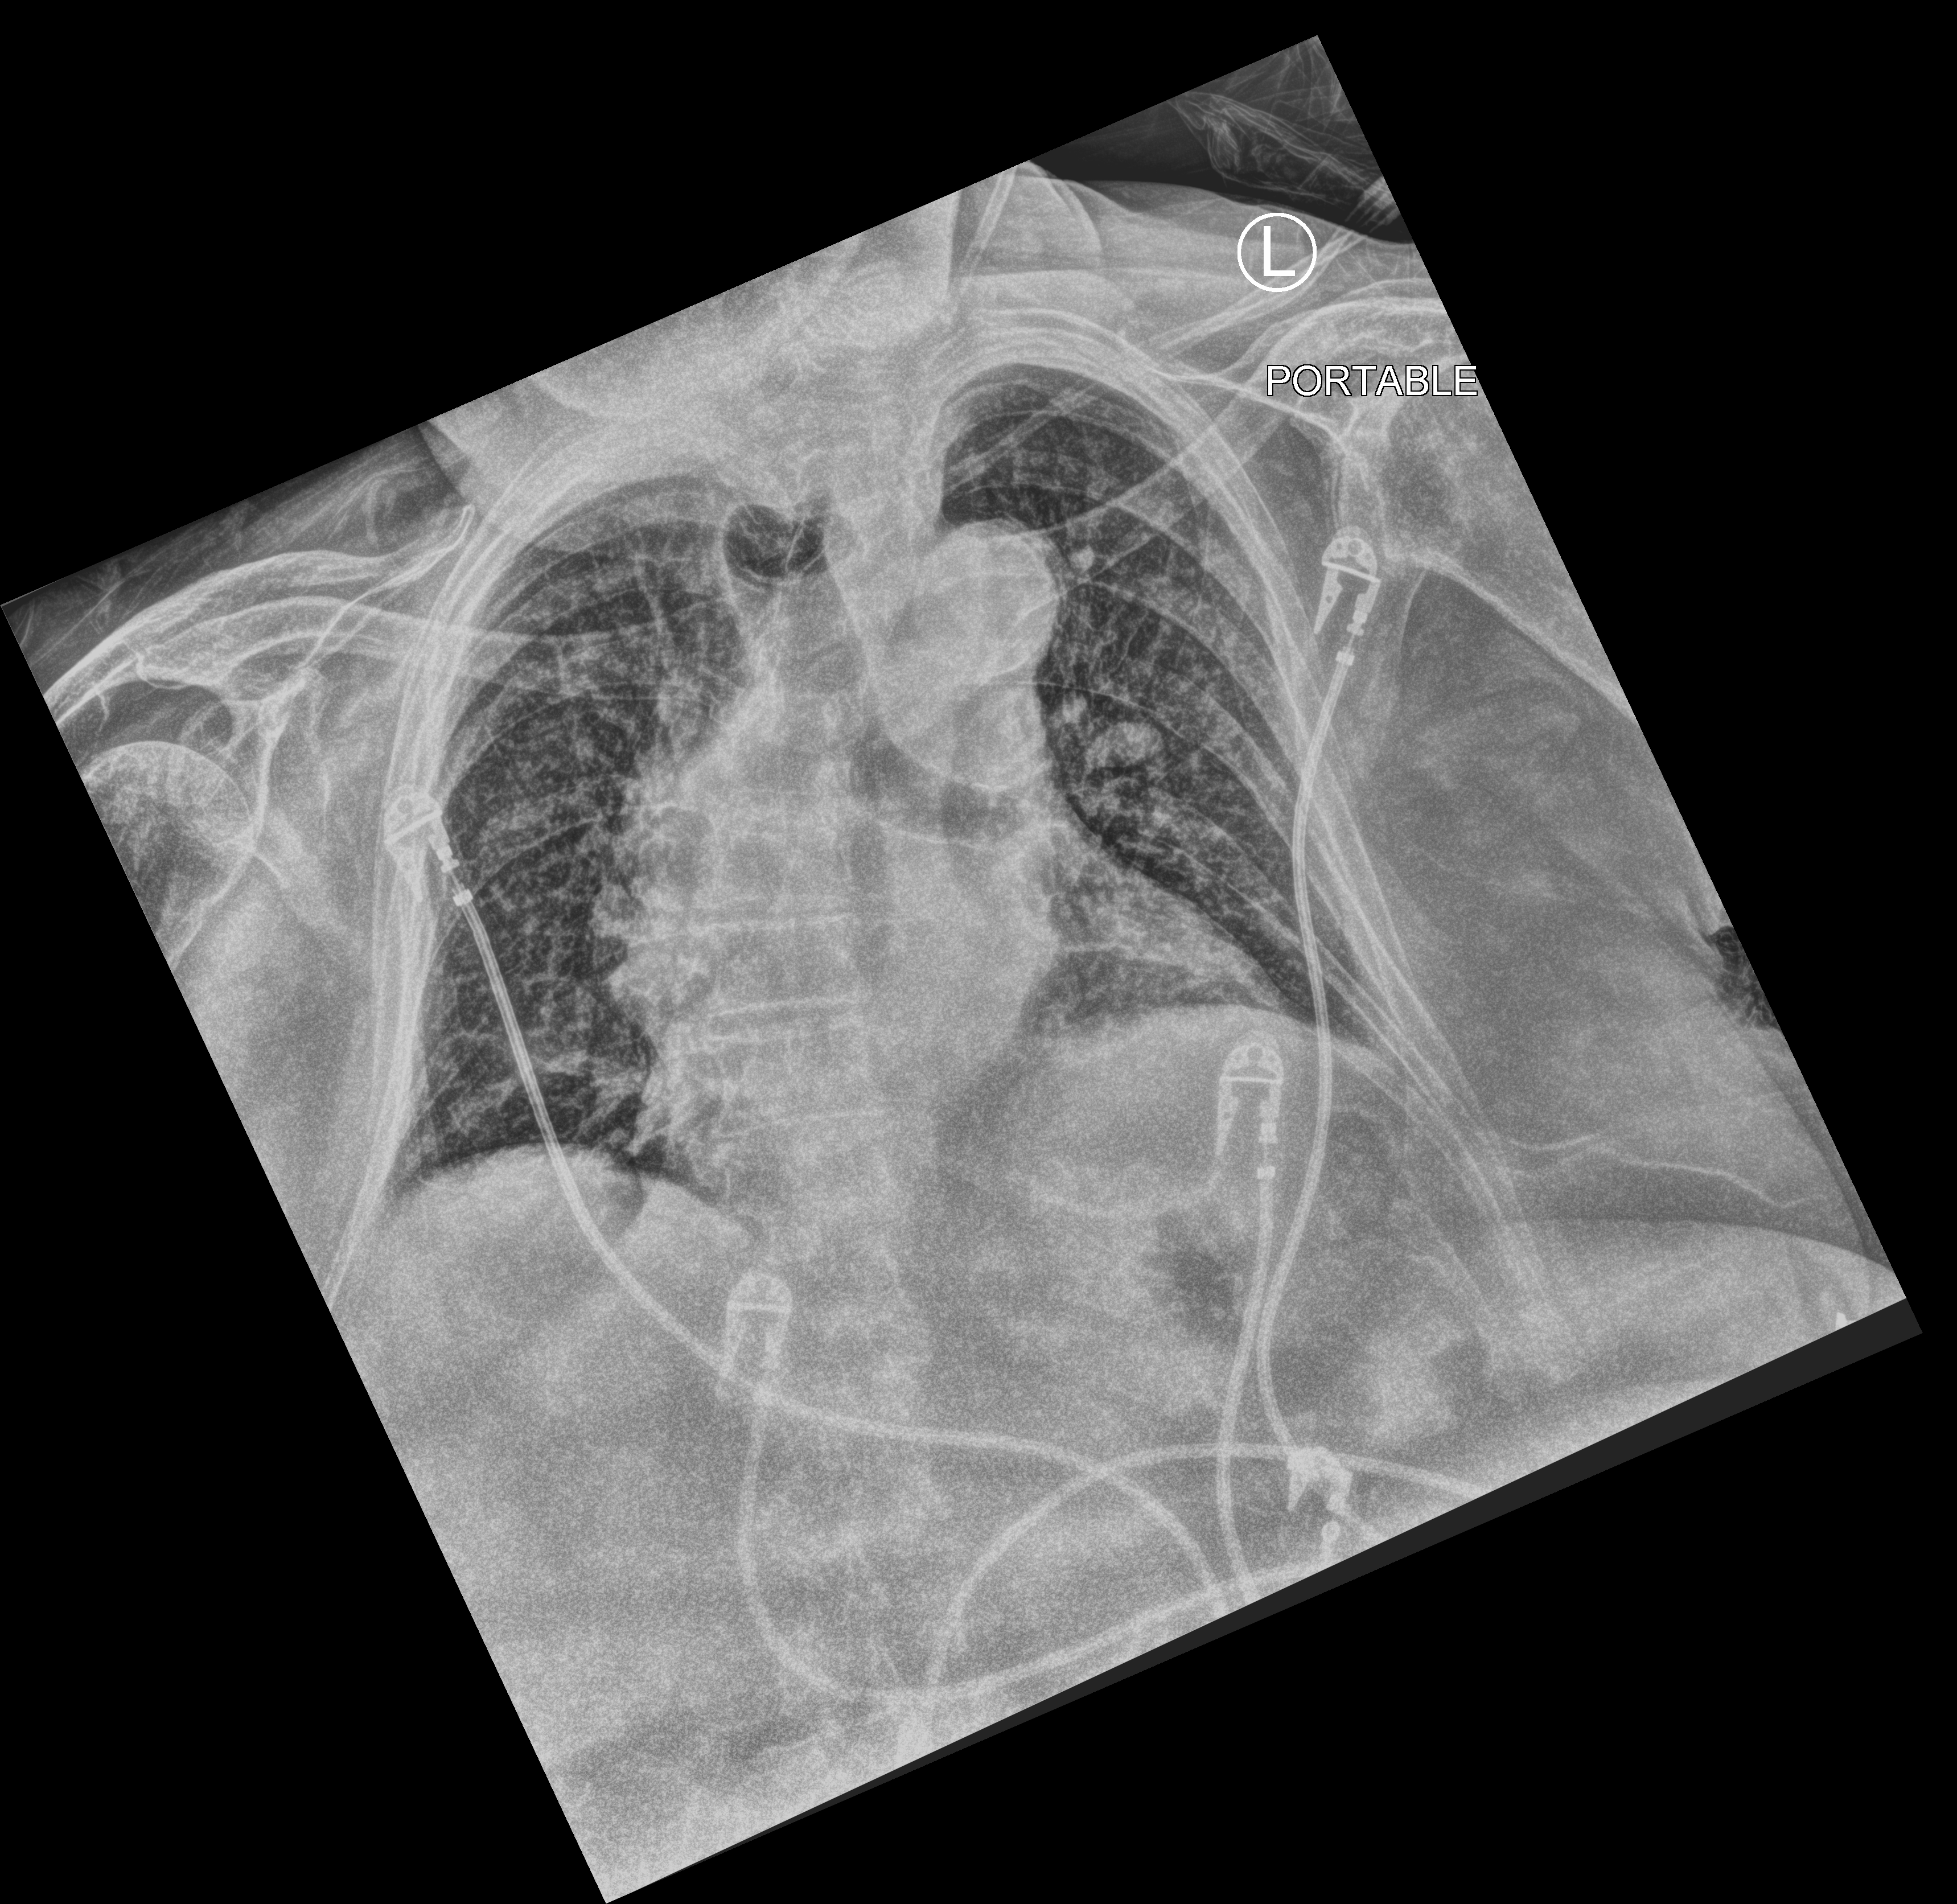
Bedside chest radiograph (computed radiography), anteroposterior (AP) projection. Female patient hospitalised with COVID-19, age 75–90 years.
Admission-level facts for this patient (not findings on this image; timing relative to this image not recorded):
- mechanically ventilated during this hospital stay: no